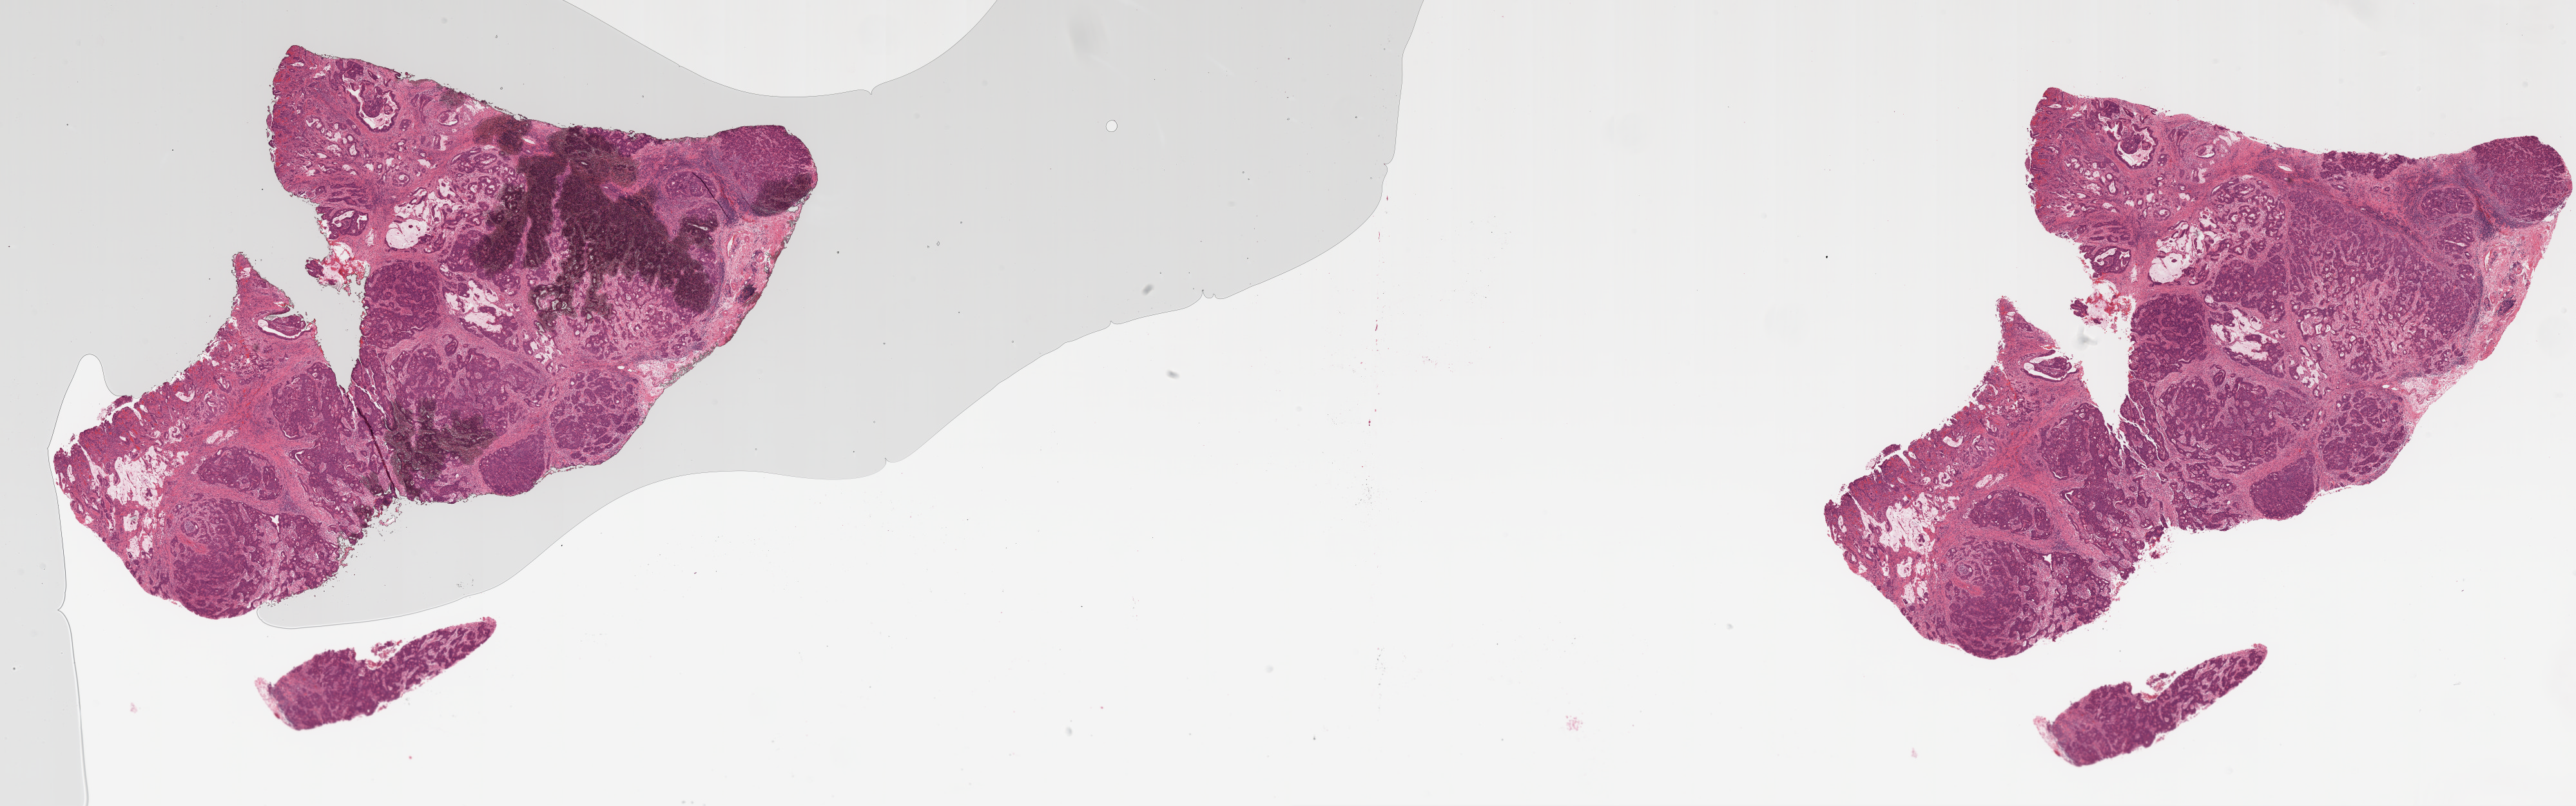
Whole-slide histology image, H&E-stained, whole scanned area (about 32.0 x 10.0 mm, slide scanned at 20x) shown as a low-resolution overview, formalin-fixed paraffin-embedded (FFPE) diagnostic section, sample: primary tumour, stomach. Male patient. Histologic grade: G2 (moderately differentiated).
Diagnosis: Mucinous adenocarcinoma (gastric antrum). AJCC pathologic stage: II (6th edition).